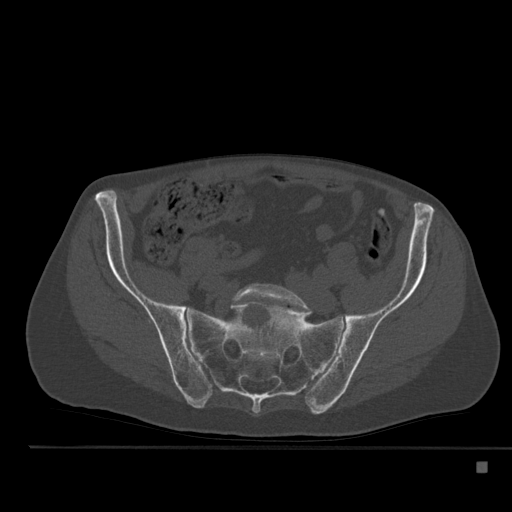
CT including the spine, one axial slice. Slice 100 of 517 in the series (ordered by position). Reconstruction kernel Br40s. Bone window (W 1800 / L 400 HU). 1.5 mm slice thickness. 512 × 512 image matrix. Patient: male, 70 years. Case-level facts recorded for this patient, not image findings: primary cancer: renal; vertebrae with lytic lesions (as recorded): T4, T6, T10, T12, L3, L4, L5.
Outlined on this slice (semi-automatic segmentation, software-assisted and operator-edited):
- L5 vertebra: bounding box (x1, y1, x2, y2) in pixels: (232, 284, 313, 312)